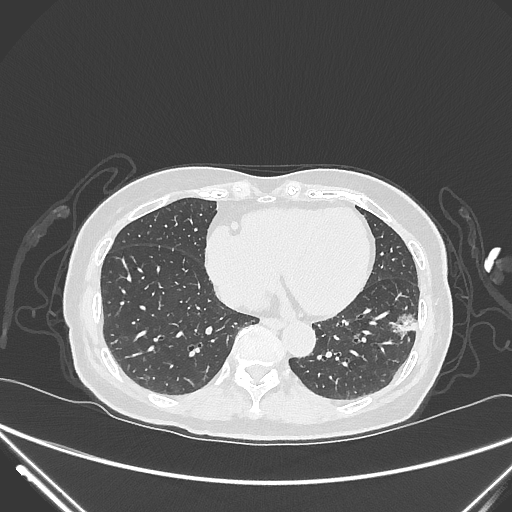
Chest CT, one axial slice; reconstruction kernel IMR1,SharpPlus; lung window (W 1500 / L -600 HU); 512 × 512 image matrix, field of view 377 × 377 mm. Female patient, age 82 years. From the clinical record (not read from this slice): clinical TNM (as recorded): T1c N0 M0.
Structures marked on this image (rectangle marked by the reading radiologist):
- lung tumour (recorded histology: adenocarcinoma): bounding box <387,308,434,355> (left, top, right, bottom; pixels)